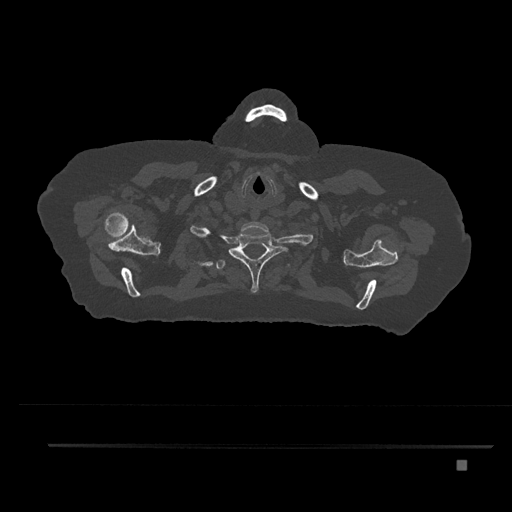
CT including the spine, one axial slice. Position 697 of 797 along the scan axis. Reconstruction kernel Br40s/3. Bone window (W 1800 / L 400 HU). 0.5 mm slice thickness. 512 × 512 image matrix, field of view 437 × 437 mm. Female patient, age 76 years. From the clinical record (not read from this slice): primary cancer: lung.
Outlined on this slice (semi-automatically segmented with operator editing):
- T1 vertebra: bounding box [x1, y1, x2, y2] px = [229, 232, 284, 293]
- T2 vertebra: [207, 247, 290, 270]